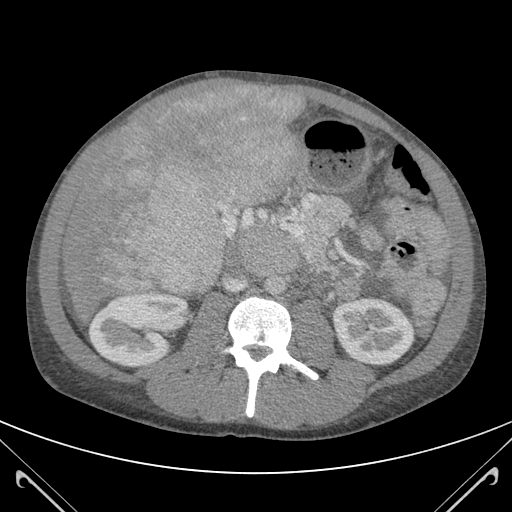
Contrast-enhanced abdominal CT (liver protocol), one axial slice. Slice 49 of 118 in the series (ordered by position). 120 kVp. Soft-tissue window (W 400 / L 40 HU). 3 mm slice thickness. 512 × 512 image matrix. From the clinical record (not read from this slice): diagnosis: hepatocellular carcinoma (patient treated with transarterial chemoembolisation; whether this scan precedes or follows treatment is not stated here); TNM stage (as recorded): Stage-IIIB; Child-Pugh class: A; tumour nodularity: uninodular.
Annotated regions visible in this slice (semi-automatic segmentation, software-assisted and operator-edited):
- abdominal aorta: bounding box [x1, y1, x2, y2] px = [265, 276, 285, 296]
- liver parenchyma outside the tumour (the mass and vessels are separate outlines, so this box may not span the whole liver): [61, 85, 303, 317]
- mass: [94, 85, 304, 297]